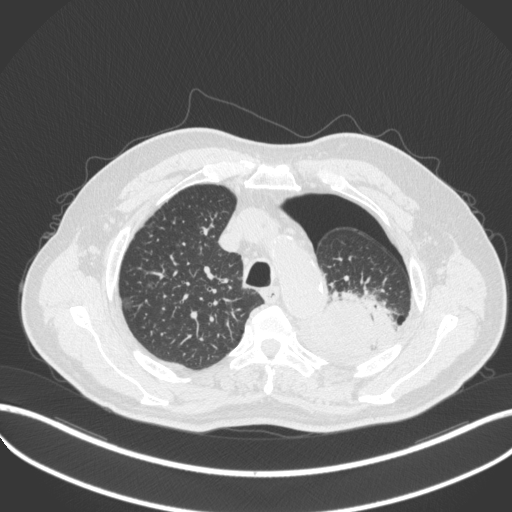
Chest CT, one axial slice. Slice 395 of 466 in the series (ordered by position). Reconstruction kernel B31f. 120 kVp. Lung window (W 1500 / L -600 HU). 1 mm slice thickness. 512 × 512 image matrix, field of view 400 × 400 mm. Male patient, age 76 years. Case-level facts recorded for this patient, not image findings: clinical TNM (as recorded): T3 N0 M1b.
Annotated regions visible in this slice (bounding box drawn by a radiologist):
- lung tumour (recorded histology: adenocarcinoma): bounding box [x1, y1, x2, y2] px = [316, 287, 395, 353]